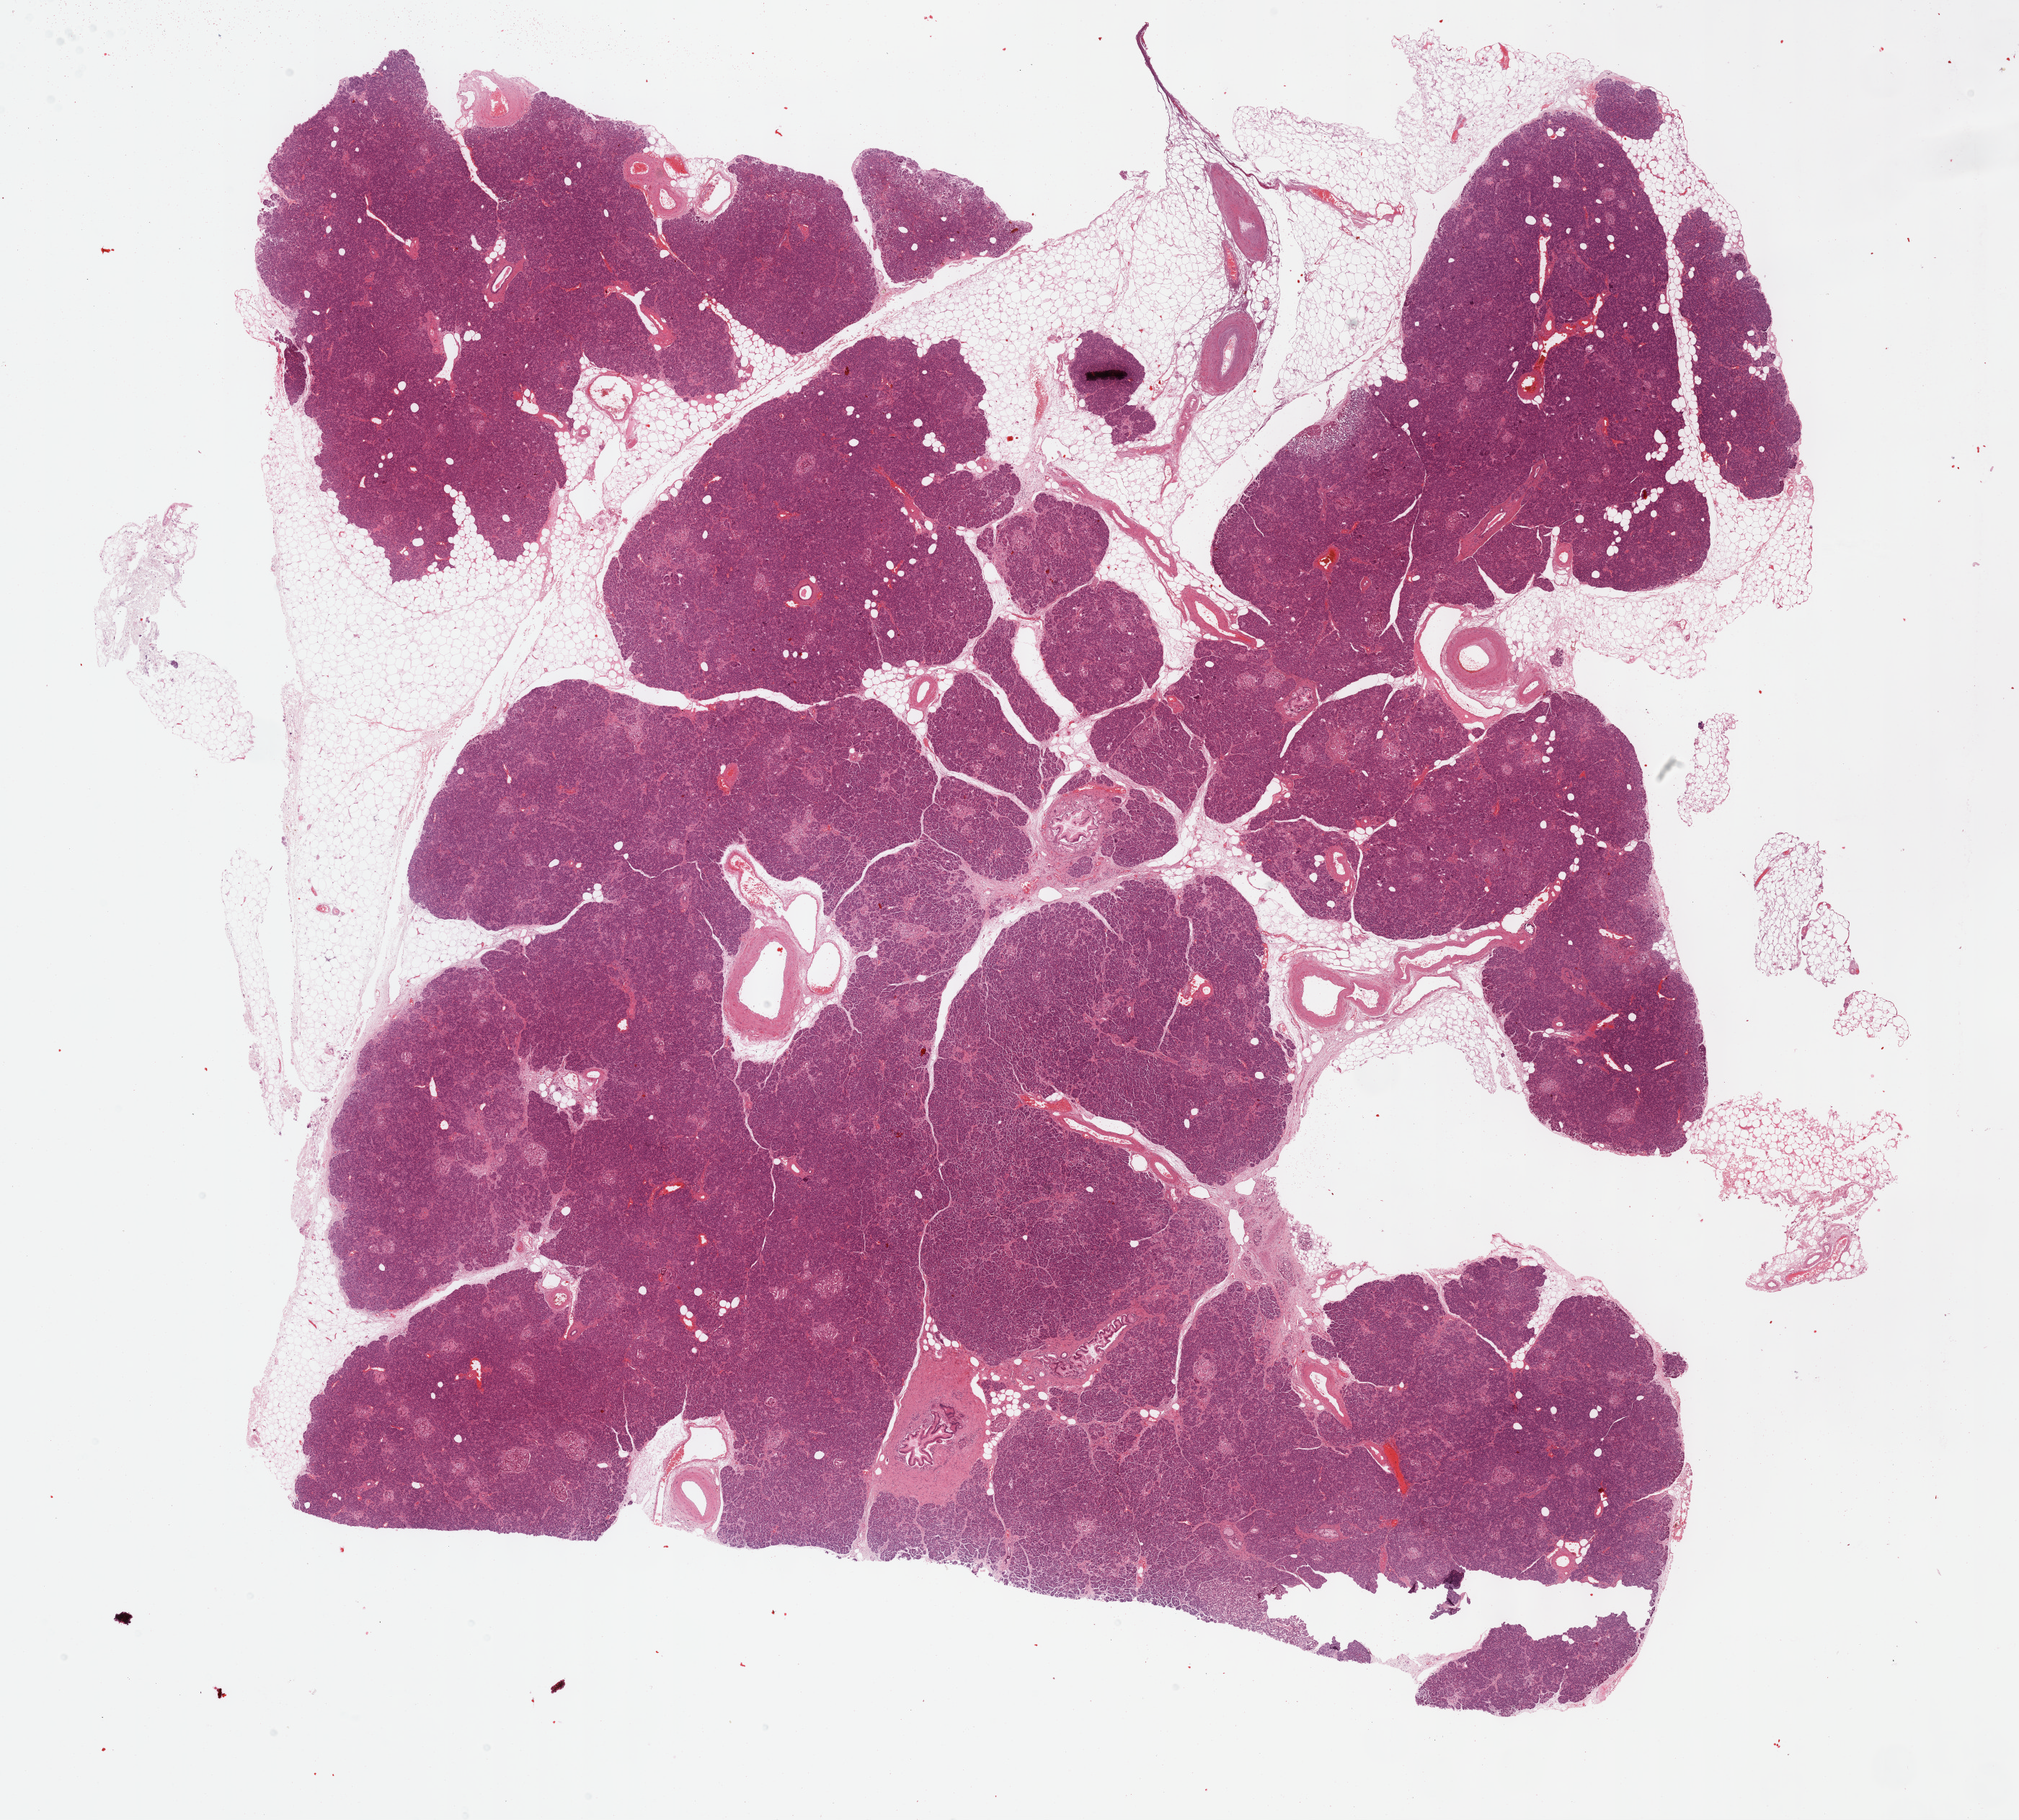
H&E whole-slide image — low-resolution overview of the scanned area, about 22.7 x 20.4 mm (acquisition: 40x scan). FFPE section. Stomach, primary tumour sample. Female, age 79 years at initial diagnosis. Histologic grade: G3 (poorly differentiated).
Pathologic diagnosis: Adenocarcinoma, intestinal type. AJCC pathologic stage: IB (7th edition). Lymph nodes positive (case pathology): 0 of 17 examined.